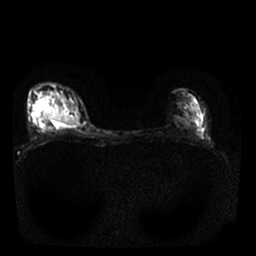
Breast MRI, one axial slice; slice 14 of 25 in the series (ordered by position); diffusion-weighted series; image 2 of 4 stored at this slice position (different b-values; order by instance number); 1.5 T; 4 mm slice thickness; 256 × 256 image matrix, field of view 310 × 310 mm. Female patient.
Outlined on this slice (expert manual segmentation):
- tumour on diffusion-weighted imaging: bounding box [x1, y1, x2, y2] px = [42, 110, 76, 125]